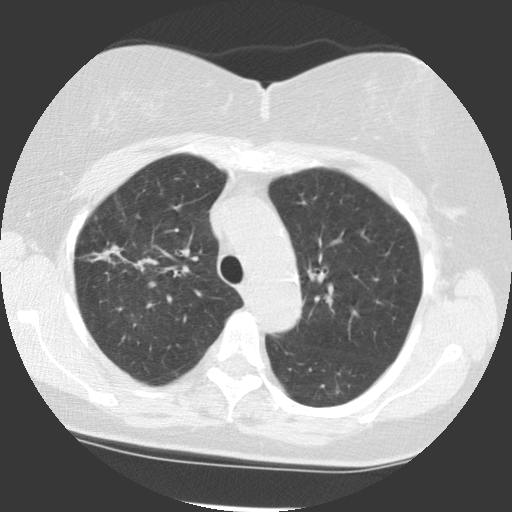
Low-dose screening chest CT, one axial slice; position 85 of 113 along the scan axis; lung window (W 1500 / L -600 HU); 2.5 mm slice thickness; 512 × 512 image matrix, field of view 320 × 320 mm.
Structures marked on this image (outlined manually by an expert reader):
- lesion 1 (tumor, upper lobe of right lung): box from (x=109, y=261) to (x=113, y=263) px